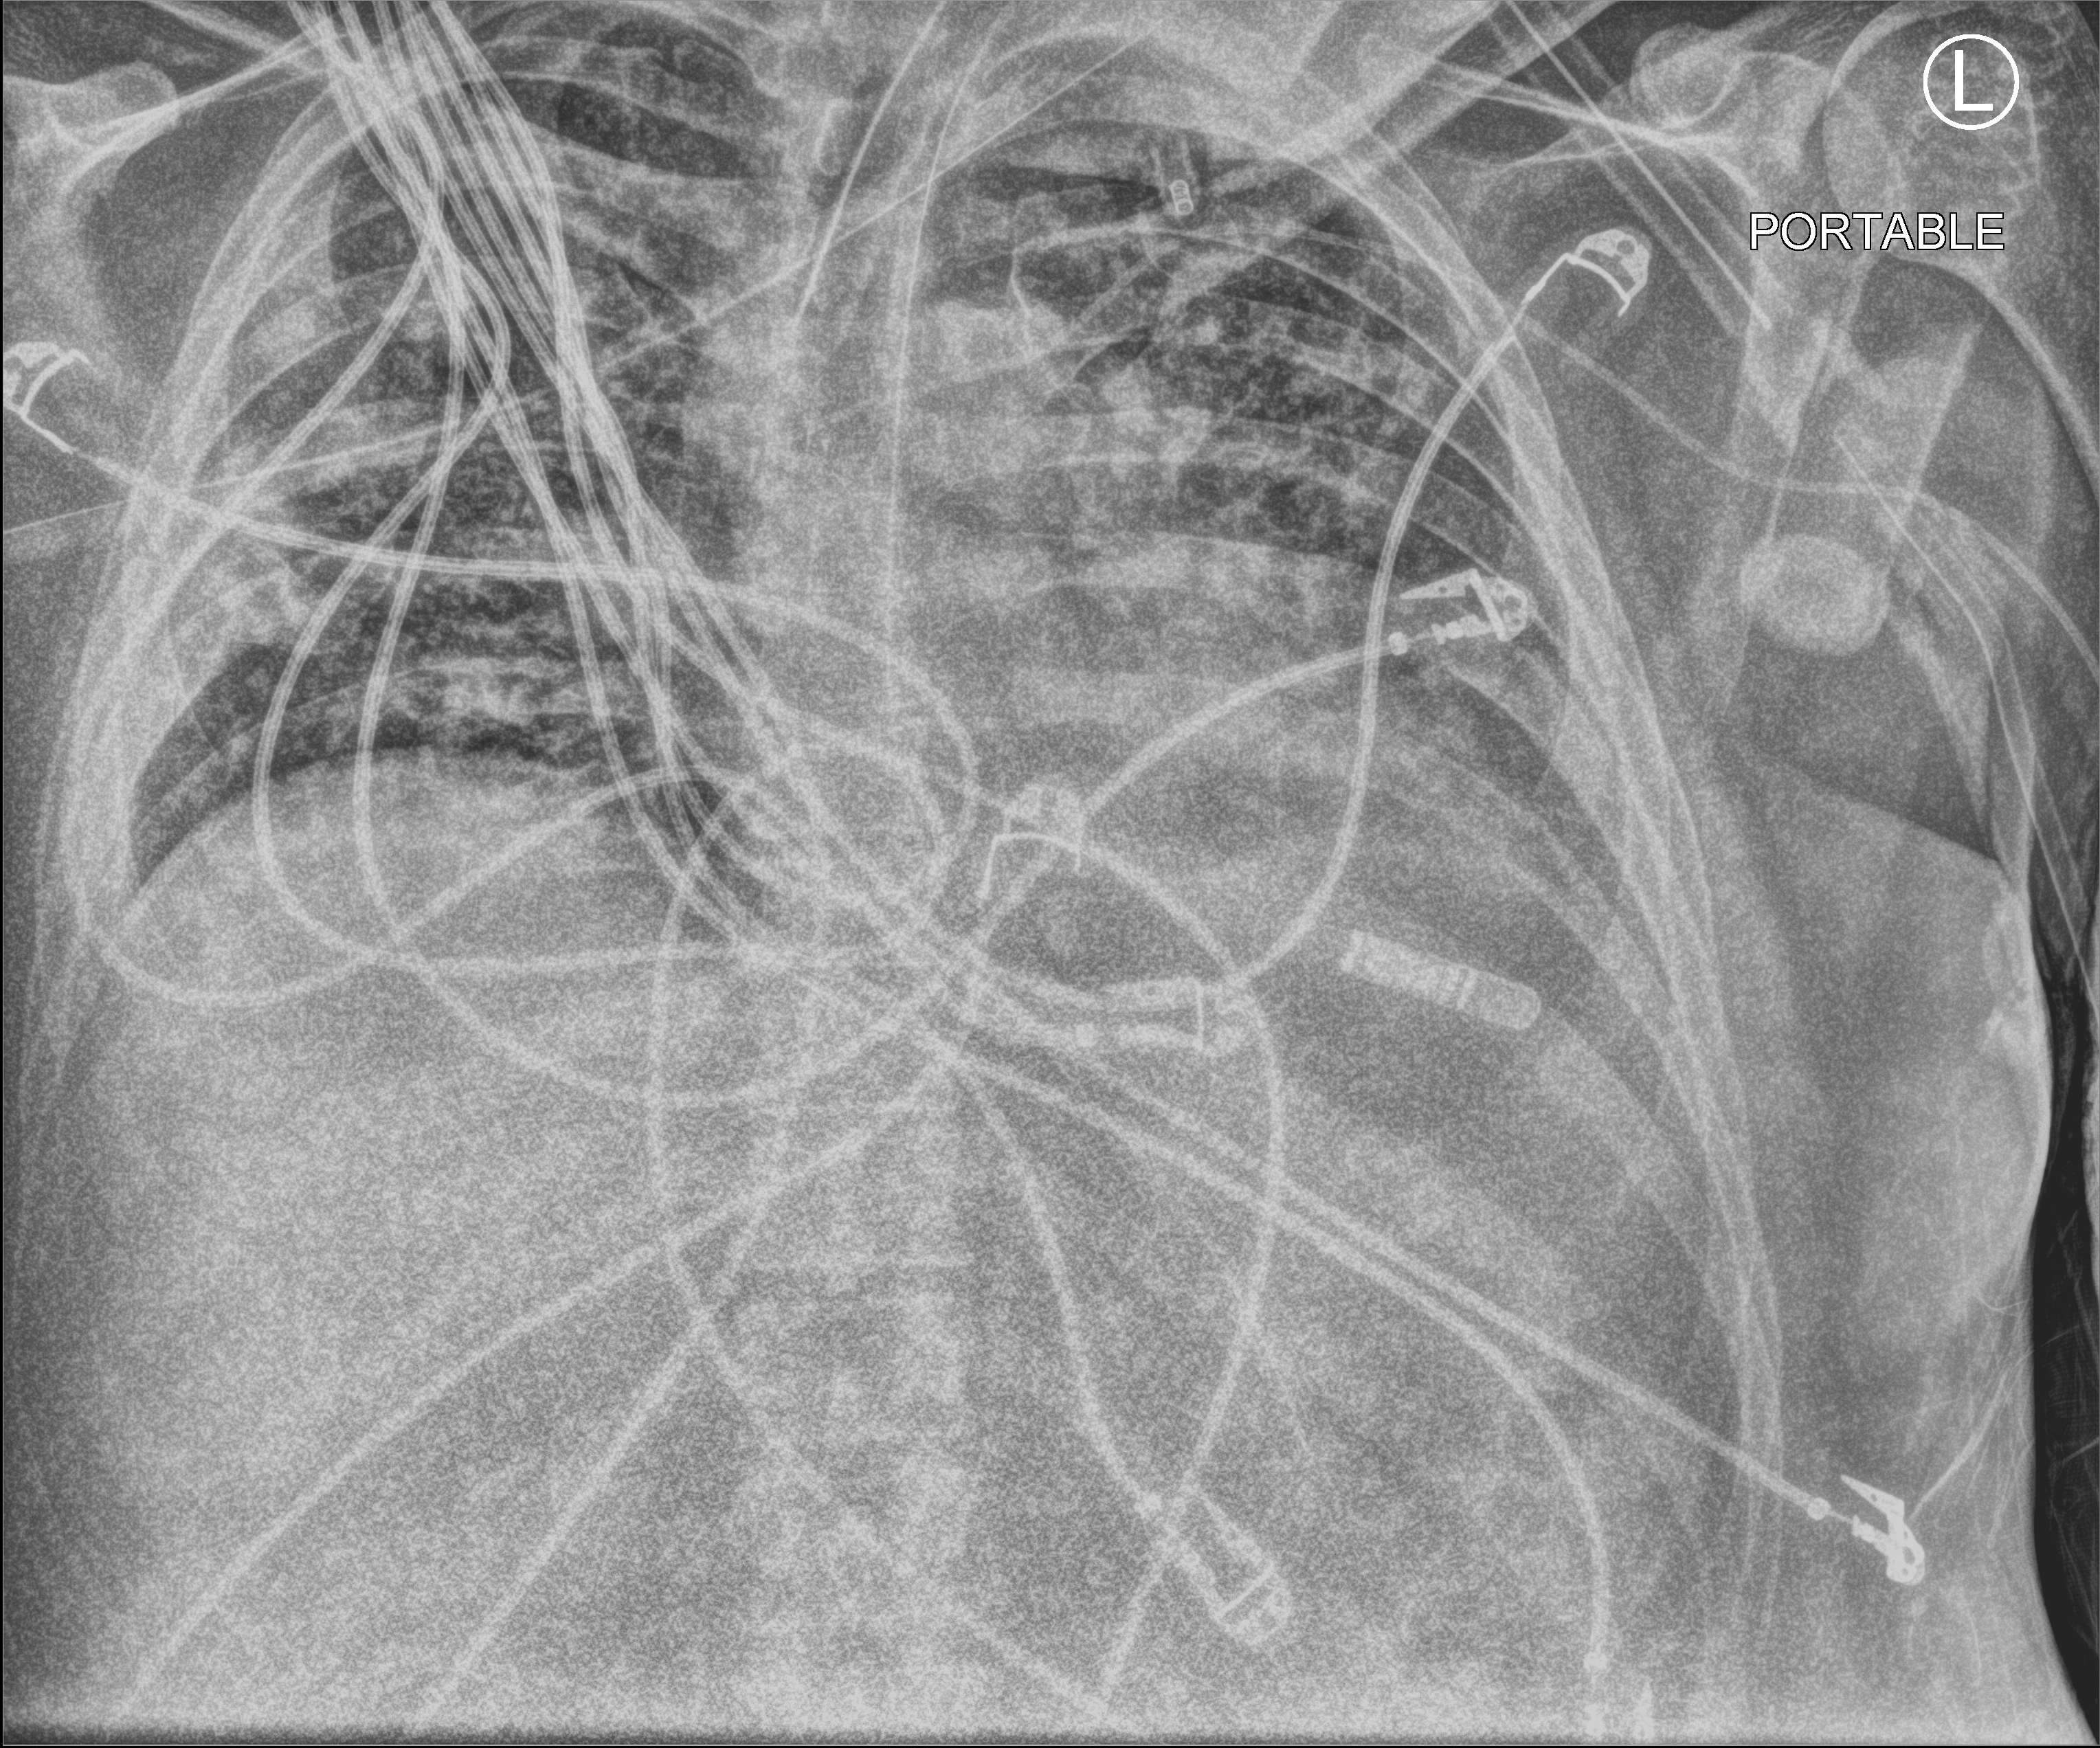
Portable chest radiograph, anteroposterior (AP) projection. Patient hospitalised with COVID-19; male, aged 18–59 years.
From the hospital-stay record, not from the radiograph (when in the stay this image was taken is not recorded):
- COPD (admission record): no
- admitted to intensive care during this hospital stay: yes
- length of hospital stay: 39 days